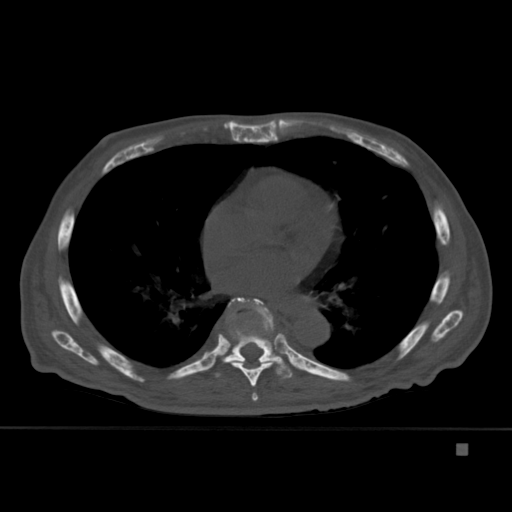
CT including the spine, one axial slice. Slice 272 of 451 in the series (ordered by position). Bone window (W 1800 / L 400 HU). 512 × 512 image matrix, field of view 378 × 378 mm. Male patient, age 75 years. Case-level facts recorded for this patient, not image findings: primary cancer: prostate.
Structures marked on this image (semi-automatically segmented with operator editing):
- T6 vertebra: box from (x=252, y=392) to (x=258, y=401) px
- T7 vertebra: (x=227, y=298)–(x=281, y=387)
- T8 vertebra: (x=209, y=297)–(x=293, y=379)